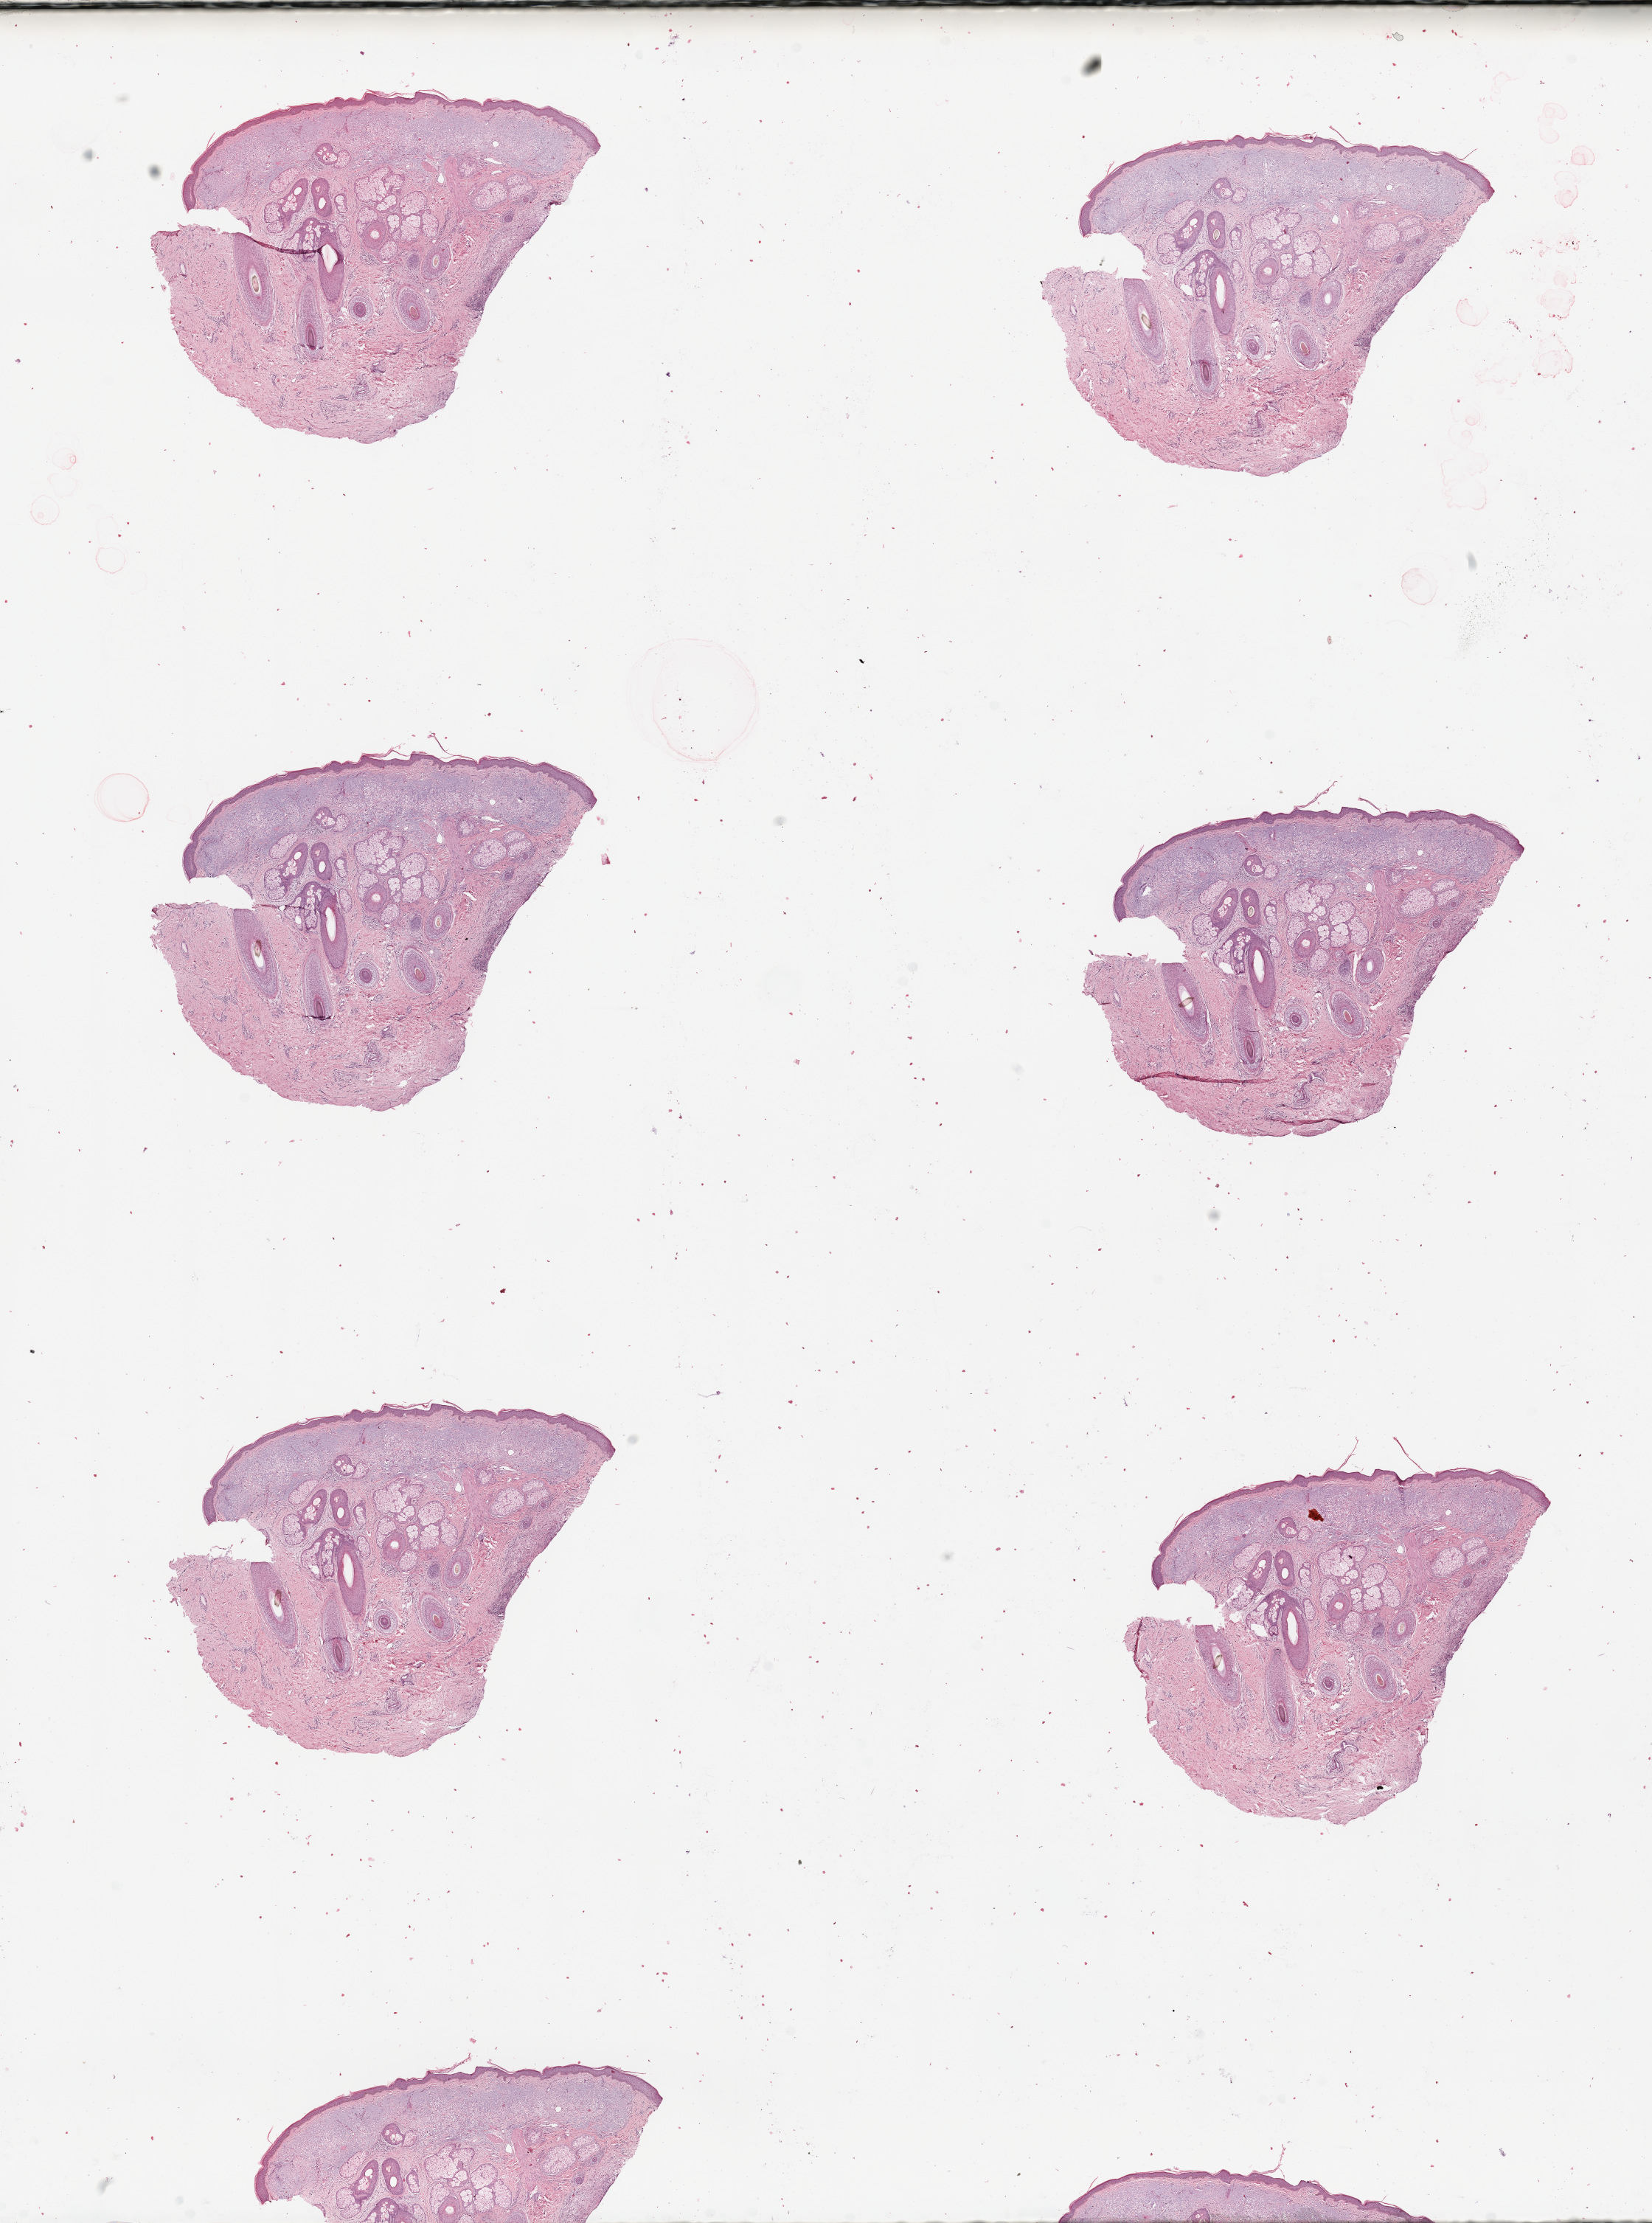
H&E-stained whole-slide image — a low-resolution overview of the entire scanned area, about 17.7 x 23.8 mm (slide scanned at 20x); normal (non-tumour) tissue sample. 68-year-old male patient.
This section: normal (non-tumour) tissue from the same patient. Patient diagnosis (cohort enrolment): sarcoma (site not recorded at cohort level).